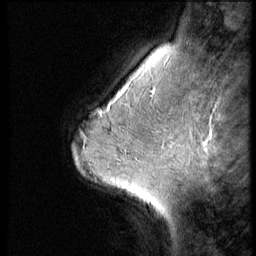
Breast MRI (dynamic contrast-enhanced), one sagittal slice. Slice 44 of 56 in the series (ordered by position). 3 images stored at this slice position (order not interpretable as contrast timing). 1.5 T. TE 4.2 ms, TR 9 ms. 256 × 256 image matrix, field of view 180 × 180 mm. Female patient, age 45 years. From the clinical record (not read from this slice): setting: breast cancer imaged before/during neoadjuvant chemotherapy; receptor status: HR-positive, HER2-negative.
Outlined on this slice (semi-automatic segmentation, software-assisted and operator-edited):
- analysis volume of interest (the breast-tissue region the enhancement analysis was run in; not a lesion): bounding box <102,77,166,129> (left, top, right, bottom; pixels)
- tumour enhancement mask (voxels above the 140 % enhancement threshold inside the analysis volume of interest): <152,91,154,94>